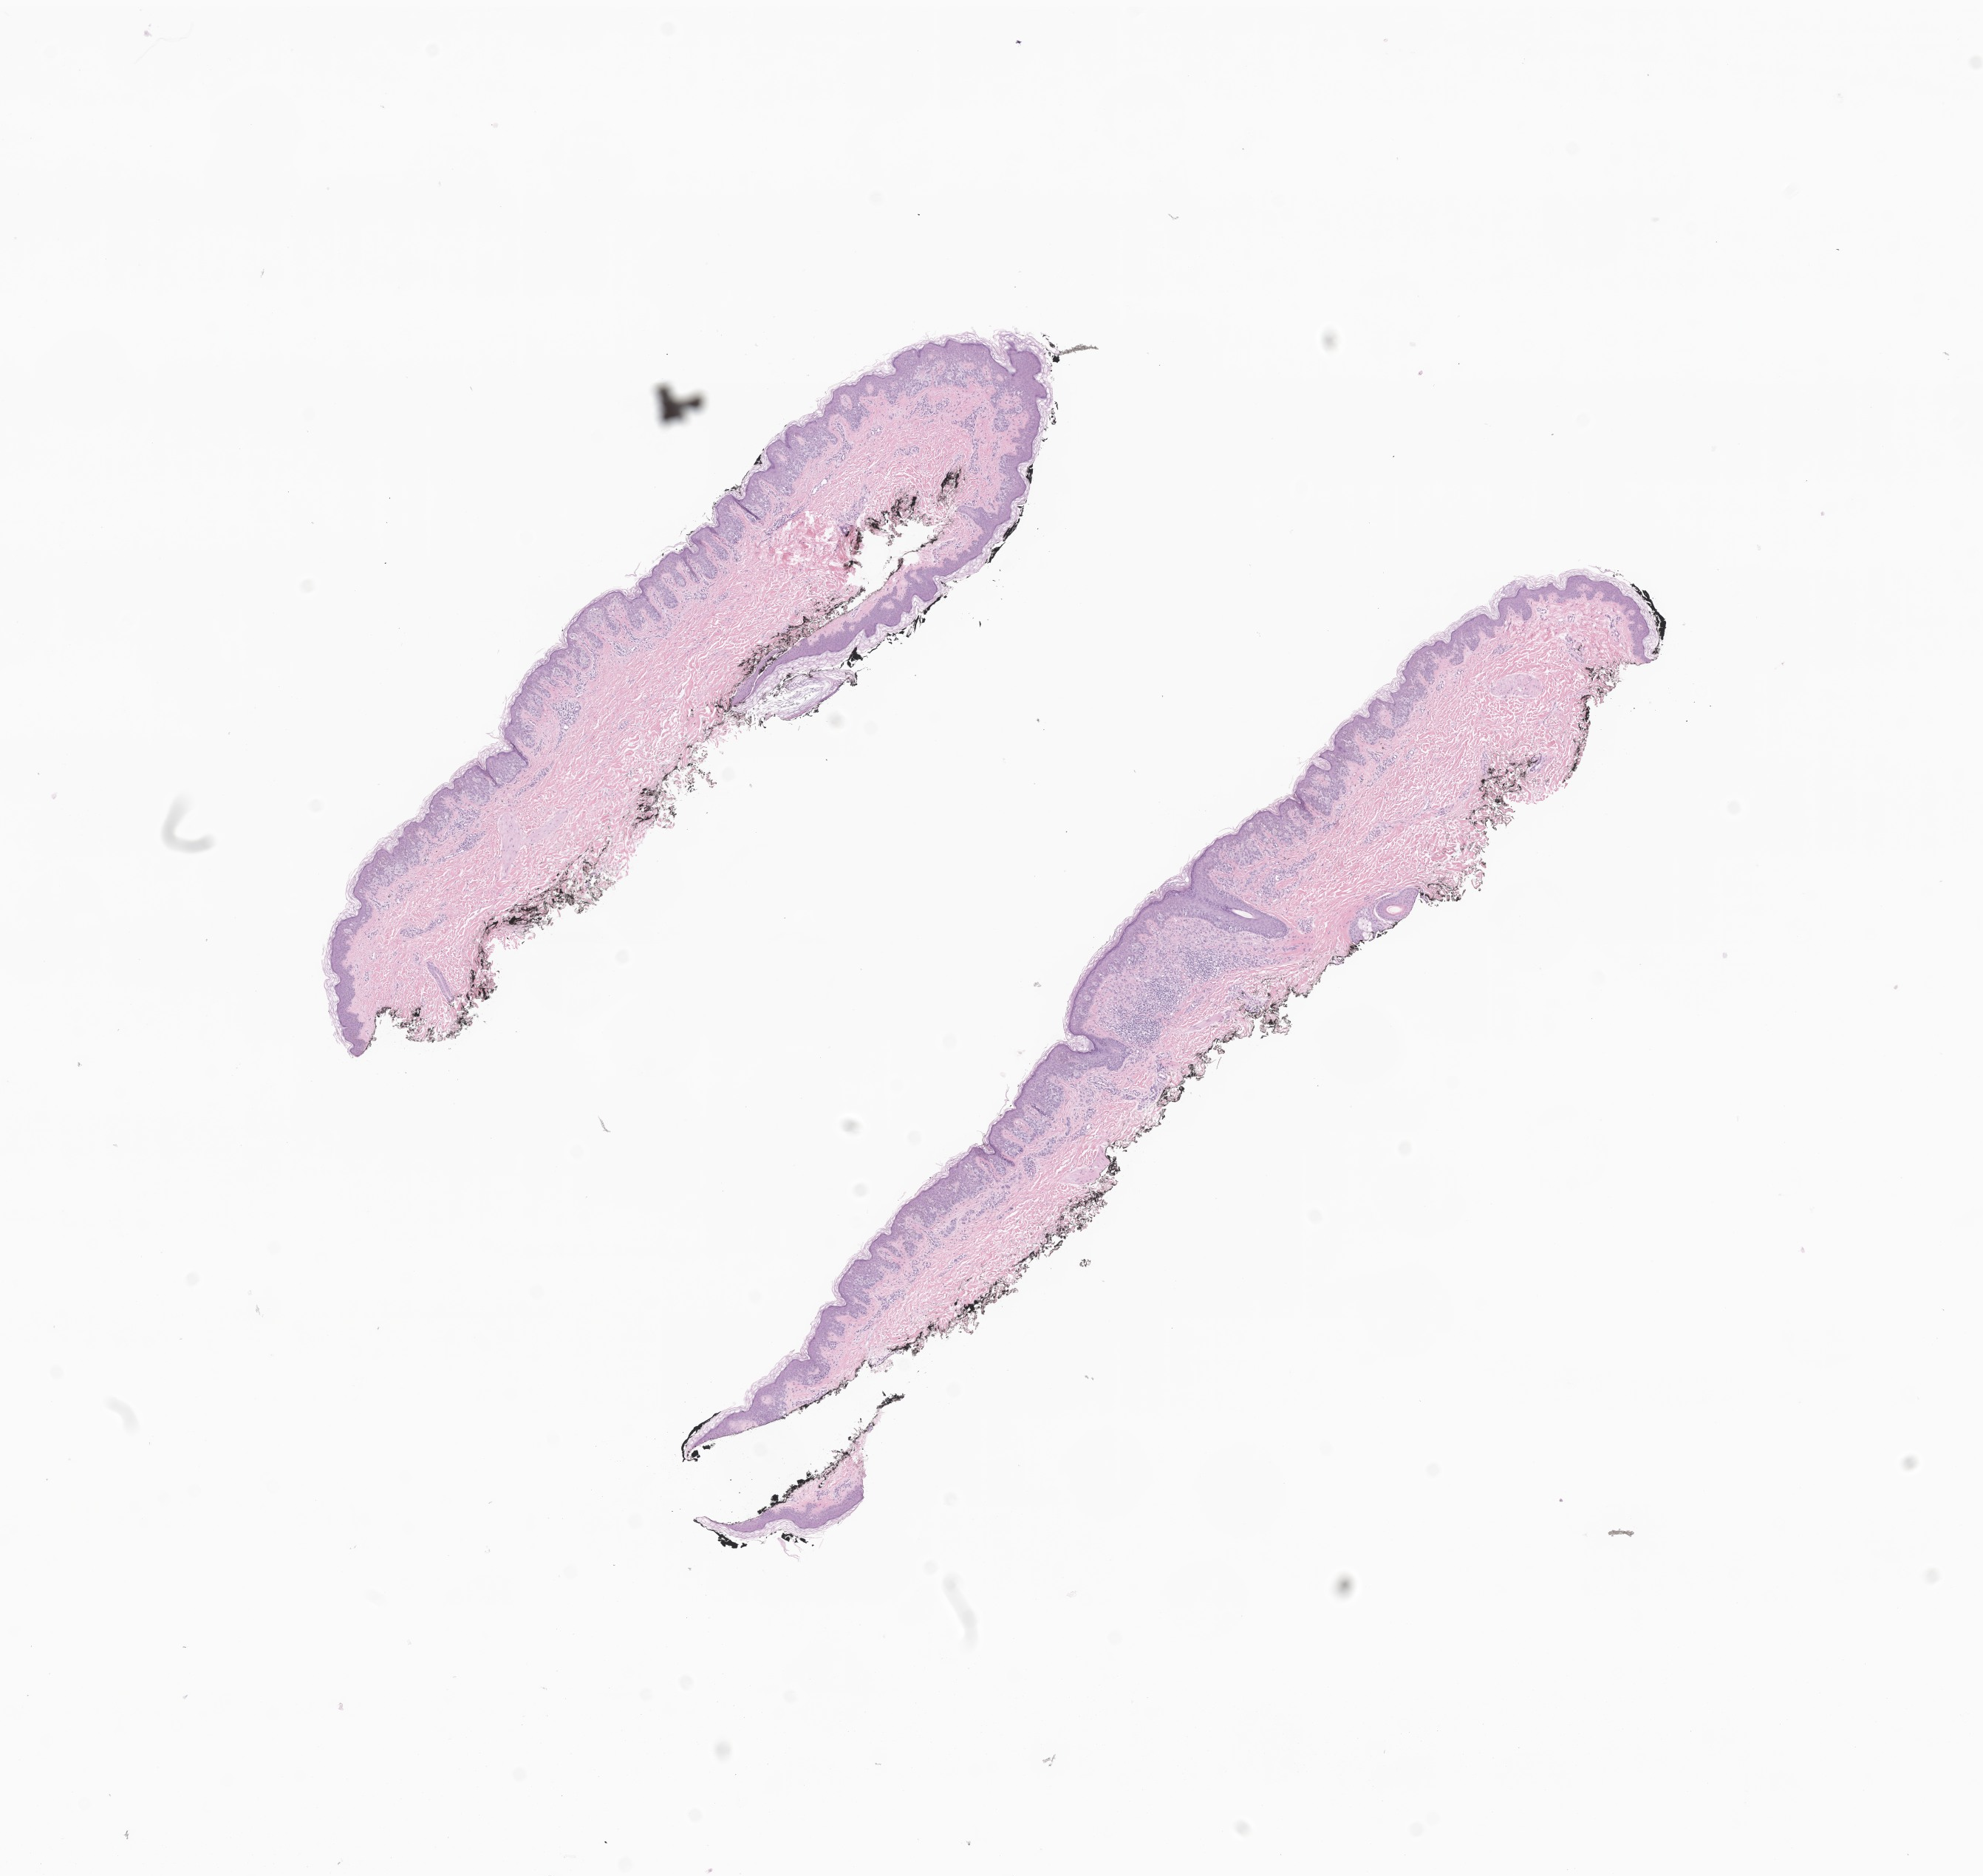
Whole-slide image, haematoxylin and eosin stain of tumor tissue from the skin of lower limb — shown as a low-resolution overview of the whole scanned area (about 11.3 x 10.7 mm). Formalin-fixed, paraffin-embedded (FFPE) tissue. Female patient, age 149 months.
Diagnosis: Malignant melanoma, NOS.